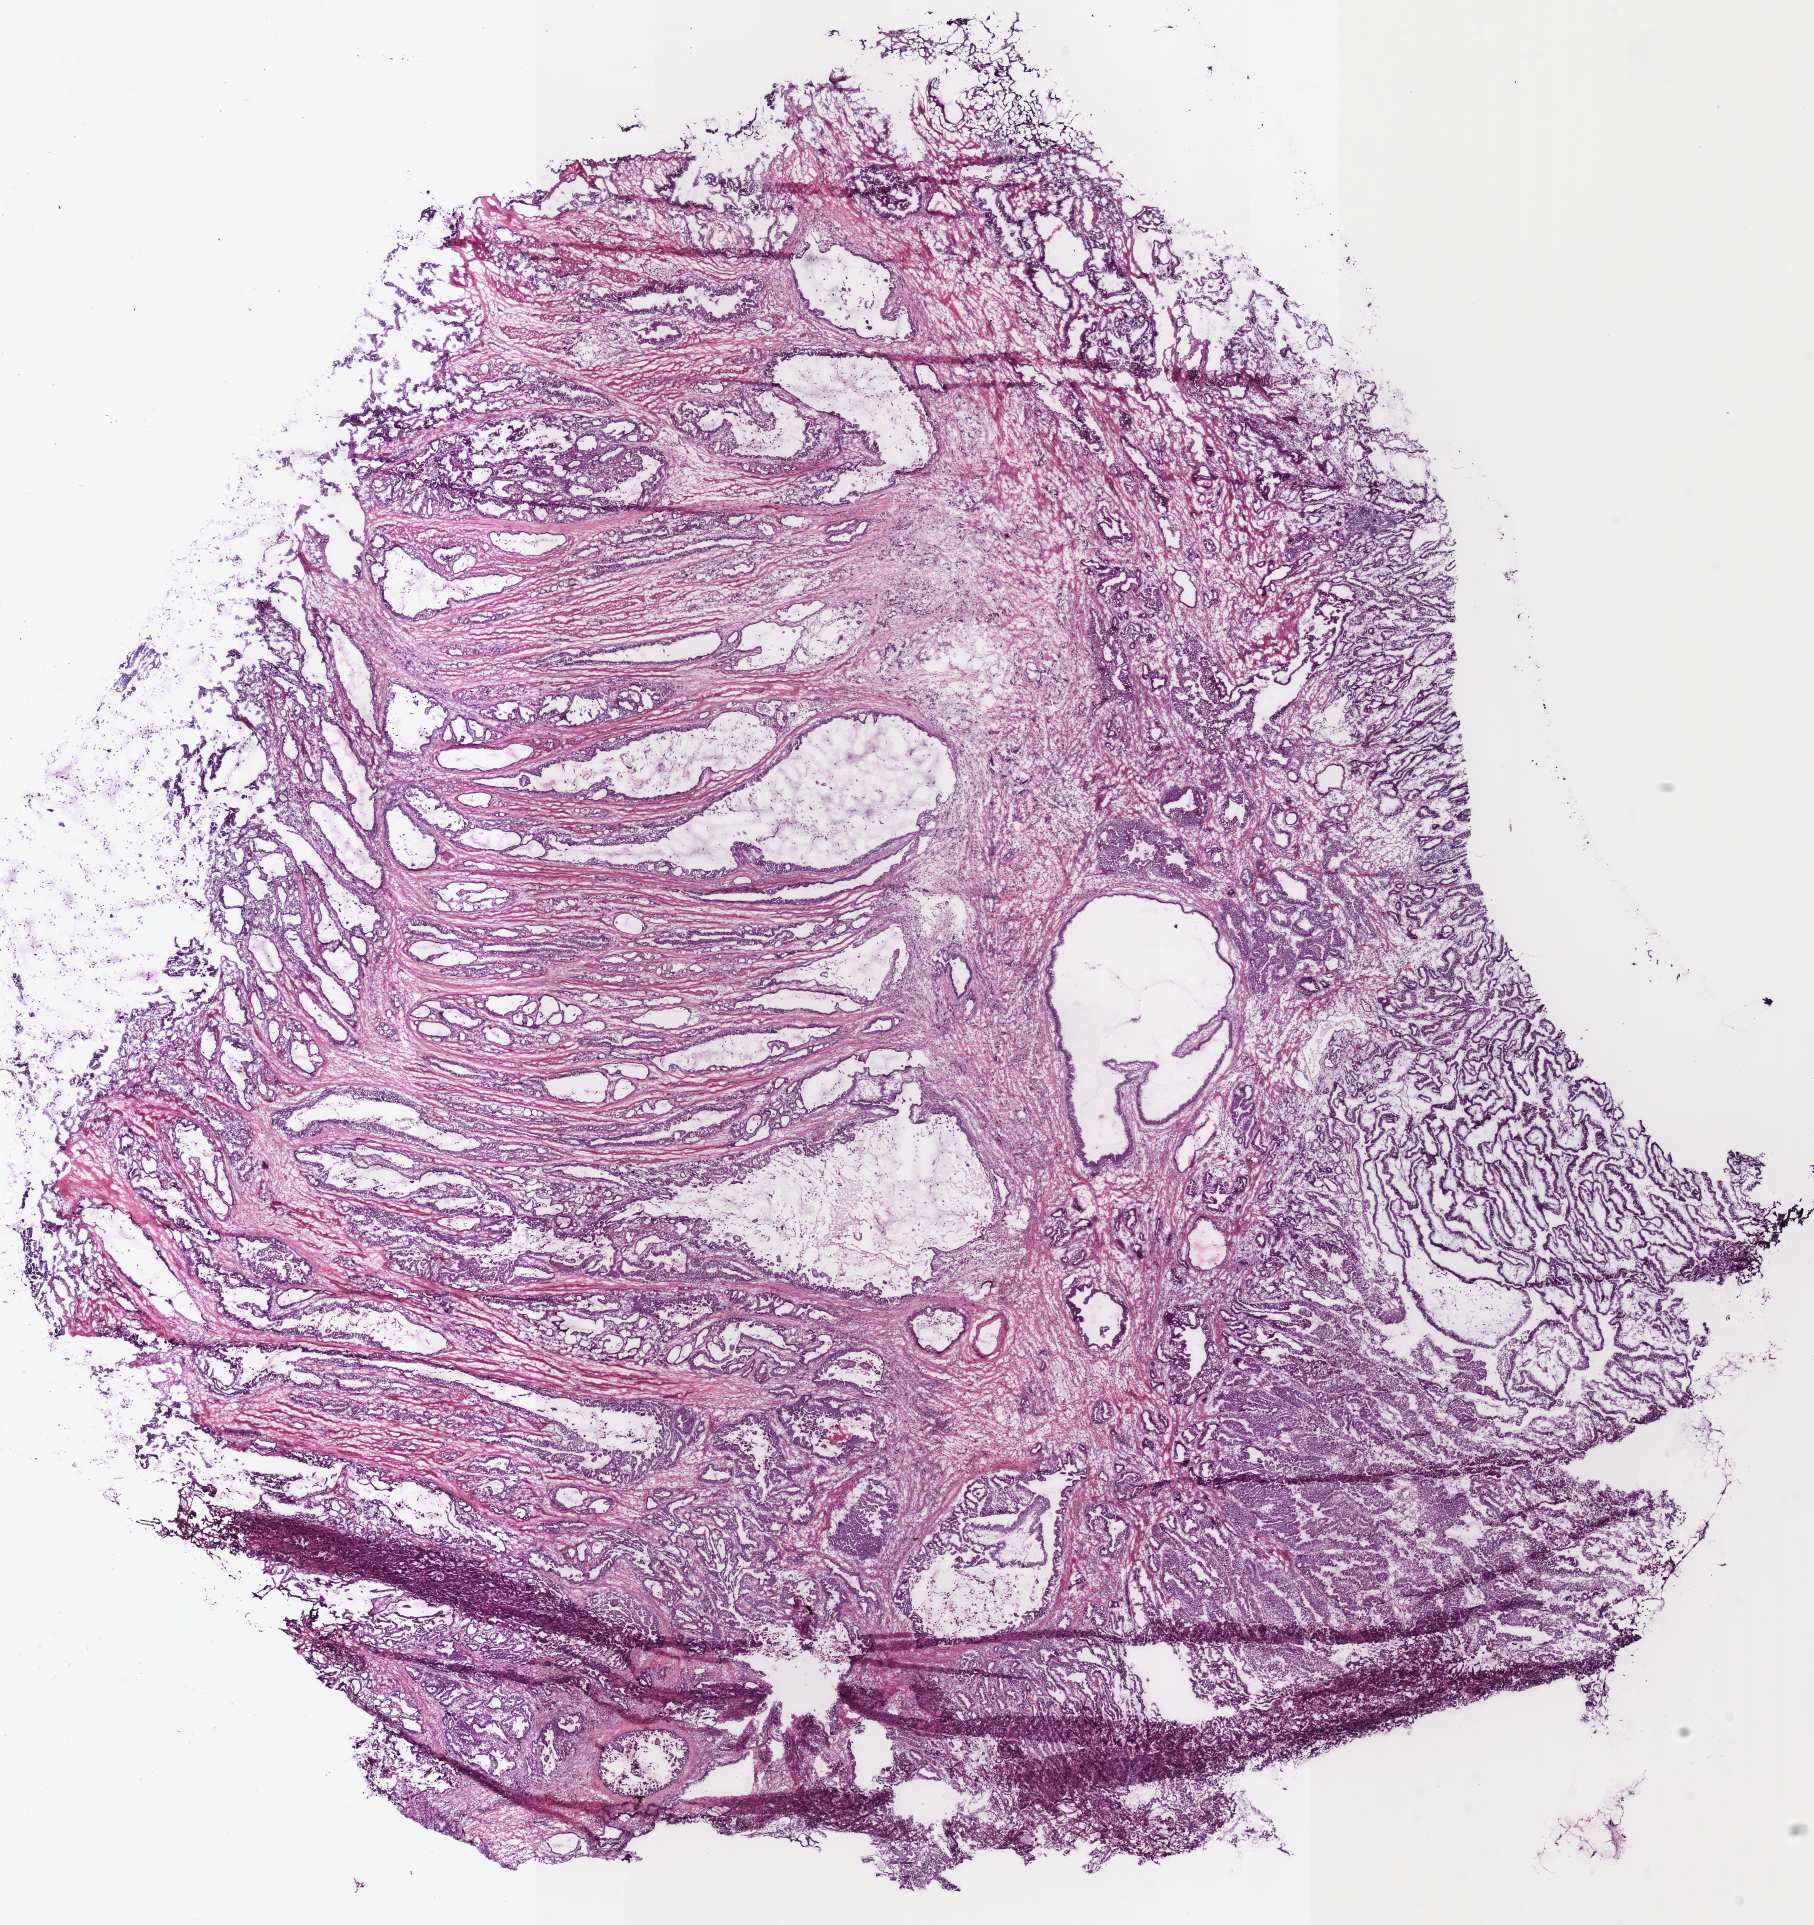
Digitized H&E tissue section (whole slide) — shown as a low-resolution overview of the whole scanned area (about 14.3 x 15.2 mm, slide scanned at 40x), frozen section from the bottom of the tissue portion, sample: primary tumour, stomach. Patient: female, age at initial diagnosis 67 years. Histologic grade: G3 (poorly differentiated). Pathologist review of this section (percent, as recorded): tumour cells 100%, tumour nuclei 80%, normal cells 0%, stromal cells 0%, necrosis 0%. Inflammatory infiltration, as recorded: lymphocyte infiltration 5%, monocyte infiltration 5%, neutrophil infiltration 5%.
Pathologic diagnosis: Adenocarcinoma, NOS (cardia, NOS). AJCC pathologic stage: IIIC.